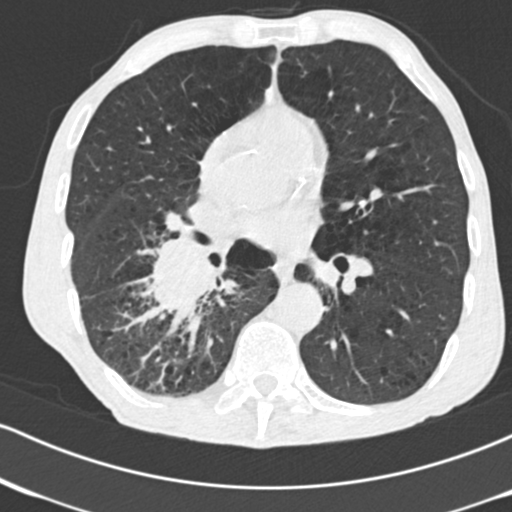
Axial slice from a low-dose chest CT screening exam. Second annual screen. Lung window (W 1500 / L -600 HU). 2 mm slice thickness. 120 kVp. 512 × 512 image matrix, field of view 316 × 316 mm. Male participant, aged 64 years at enrolment. Current smoker at enrolment.
Expert reader's lesion annotation, bounding box <126,226,241,335> (left, top, right, bottom; pixels). The exam's reader record, not a measurement of the box and not confirmed to be the same lesion: non-calcified nodule or mass ≥4 mm, 52 × 37 mm, spiculated (stellate) margins, soft tissue attenuation, pre-existing on the prior screen: no. Official screen result: positive, other. Later outcome: lung cancer diagnosed 28 days after this screen — adenocarcinoma, NOS, right lower lobe, stage IV (AJCC 6th edition), 60 mm at pathology.